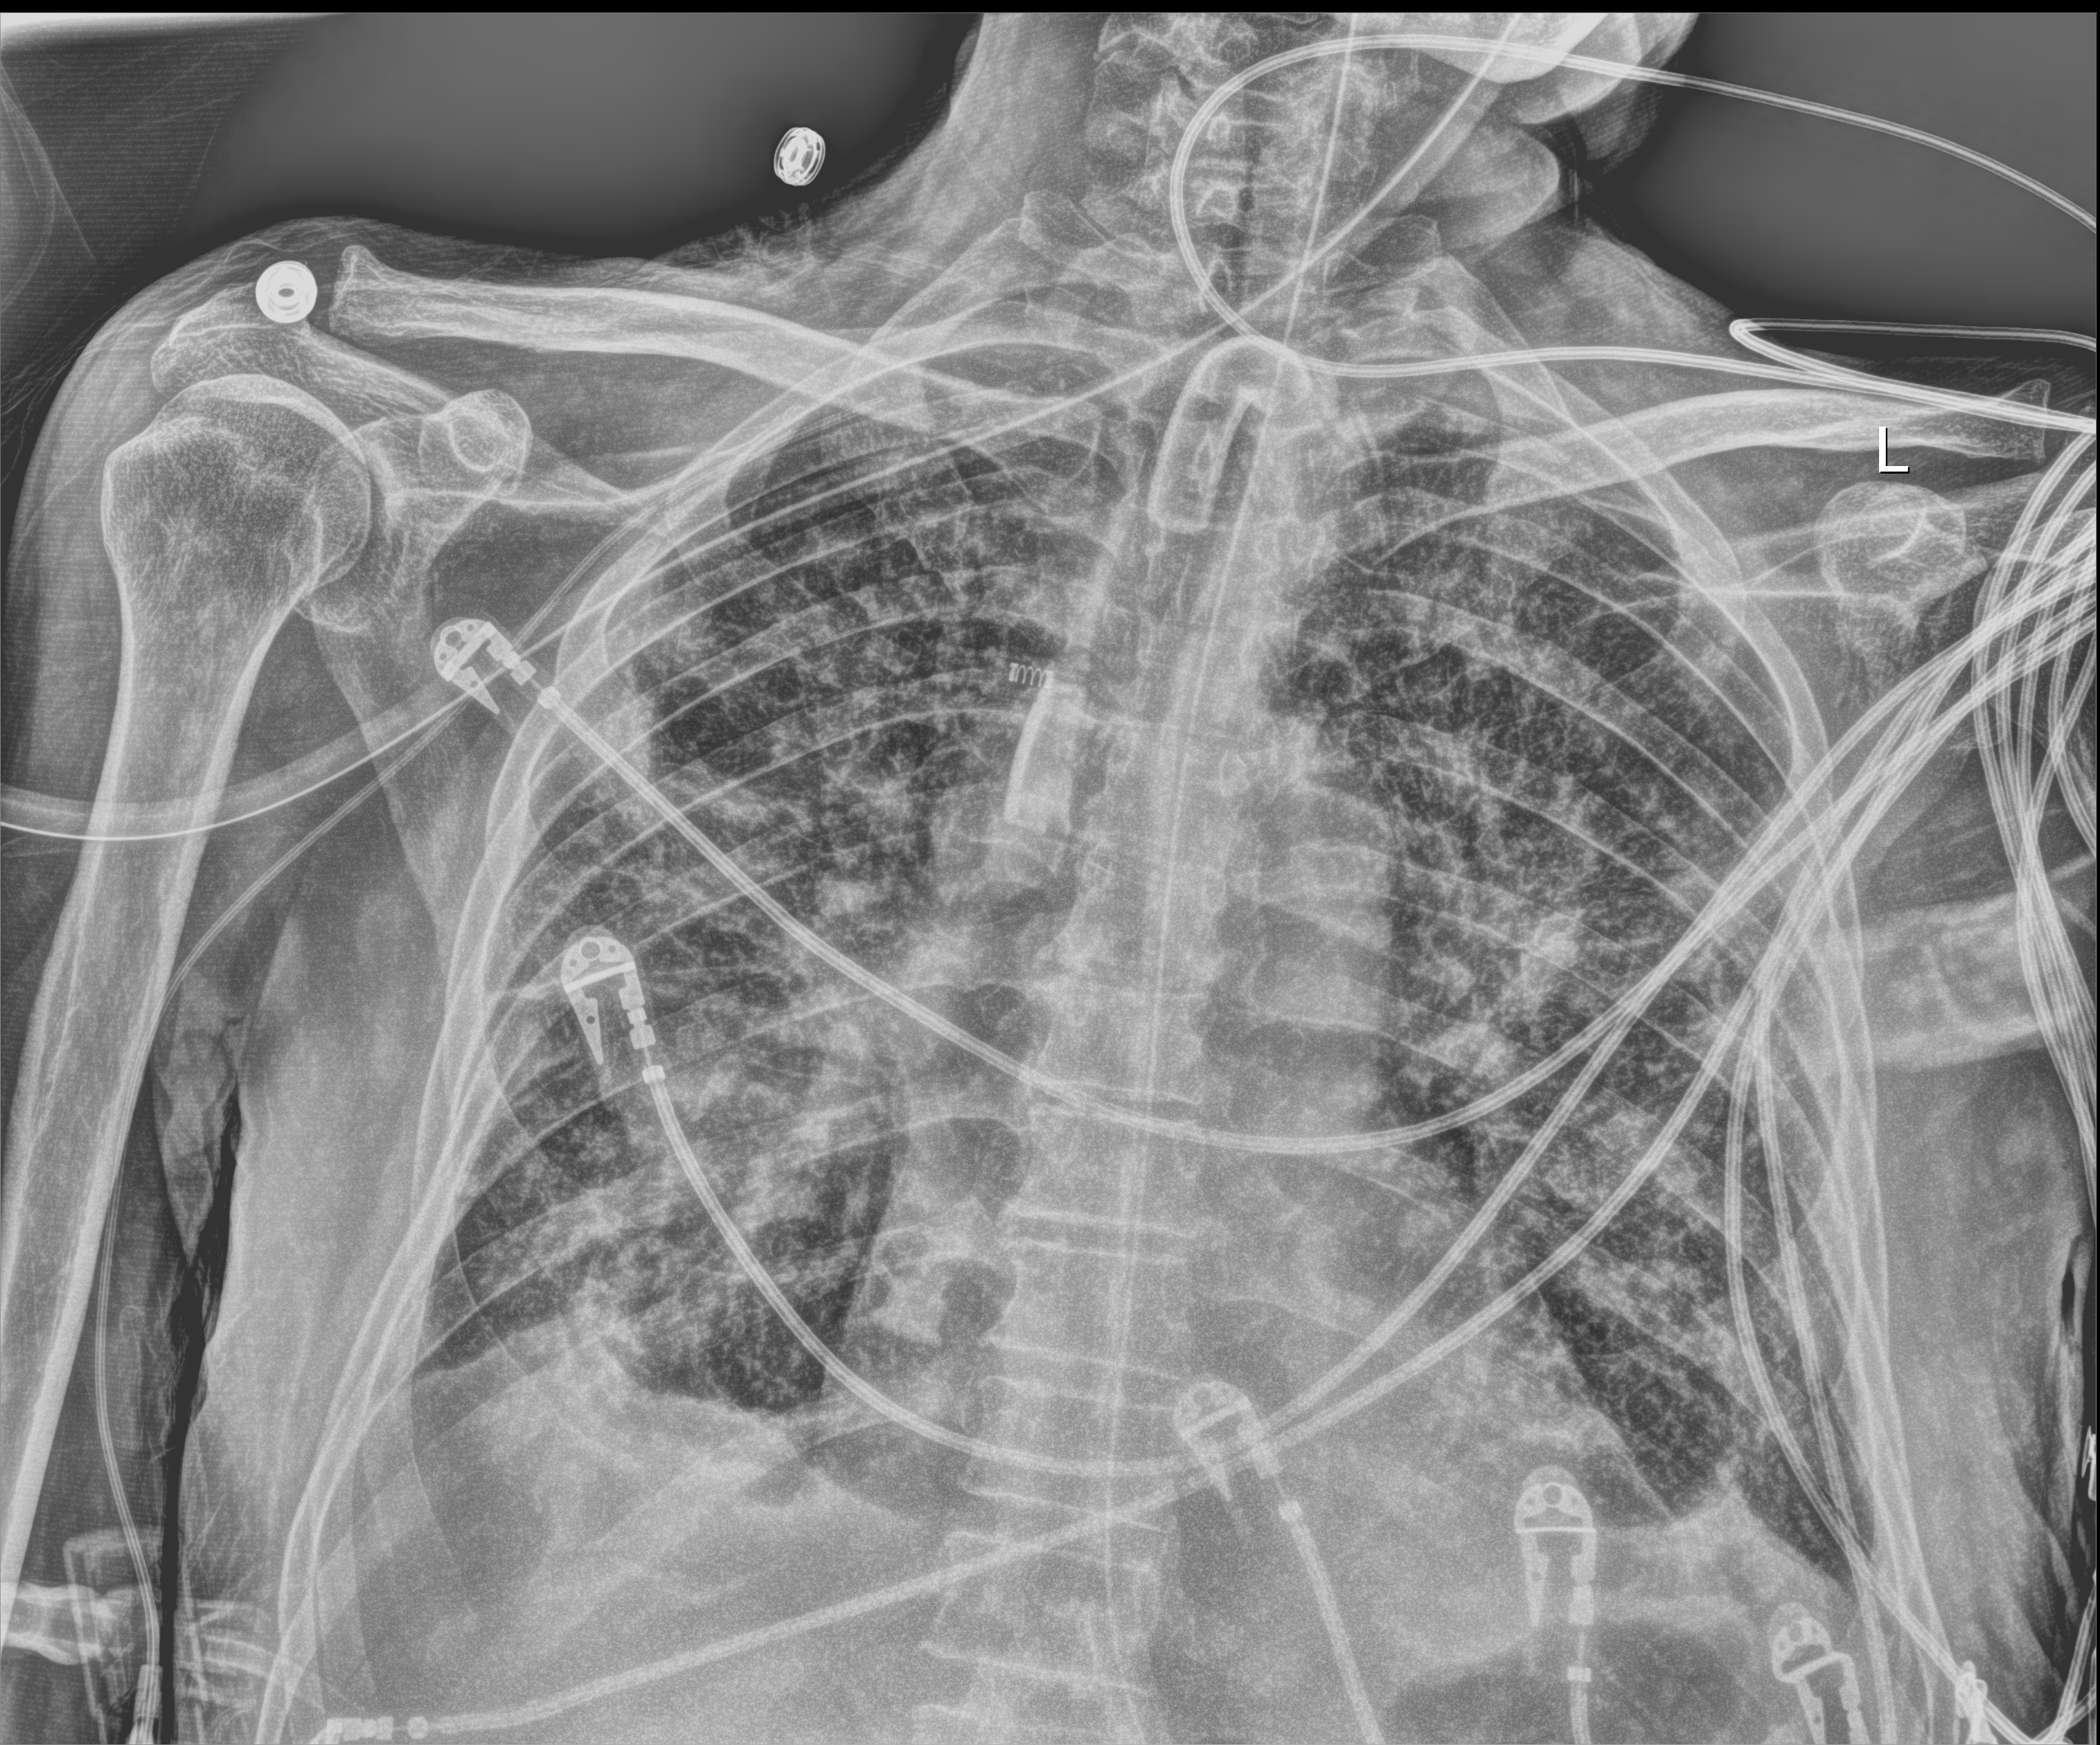
Portable chest radiograph; anteroposterior (AP) projection. Patient hospitalised with COVID-19; male, aged 75–90 years.
Admission-level facts for this patient (not findings on this image; timing relative to this image not recorded): length of hospital stay: 70 days; mechanically ventilated during this hospital stay: yes; admitted to intensive care during this hospital stay: yes.